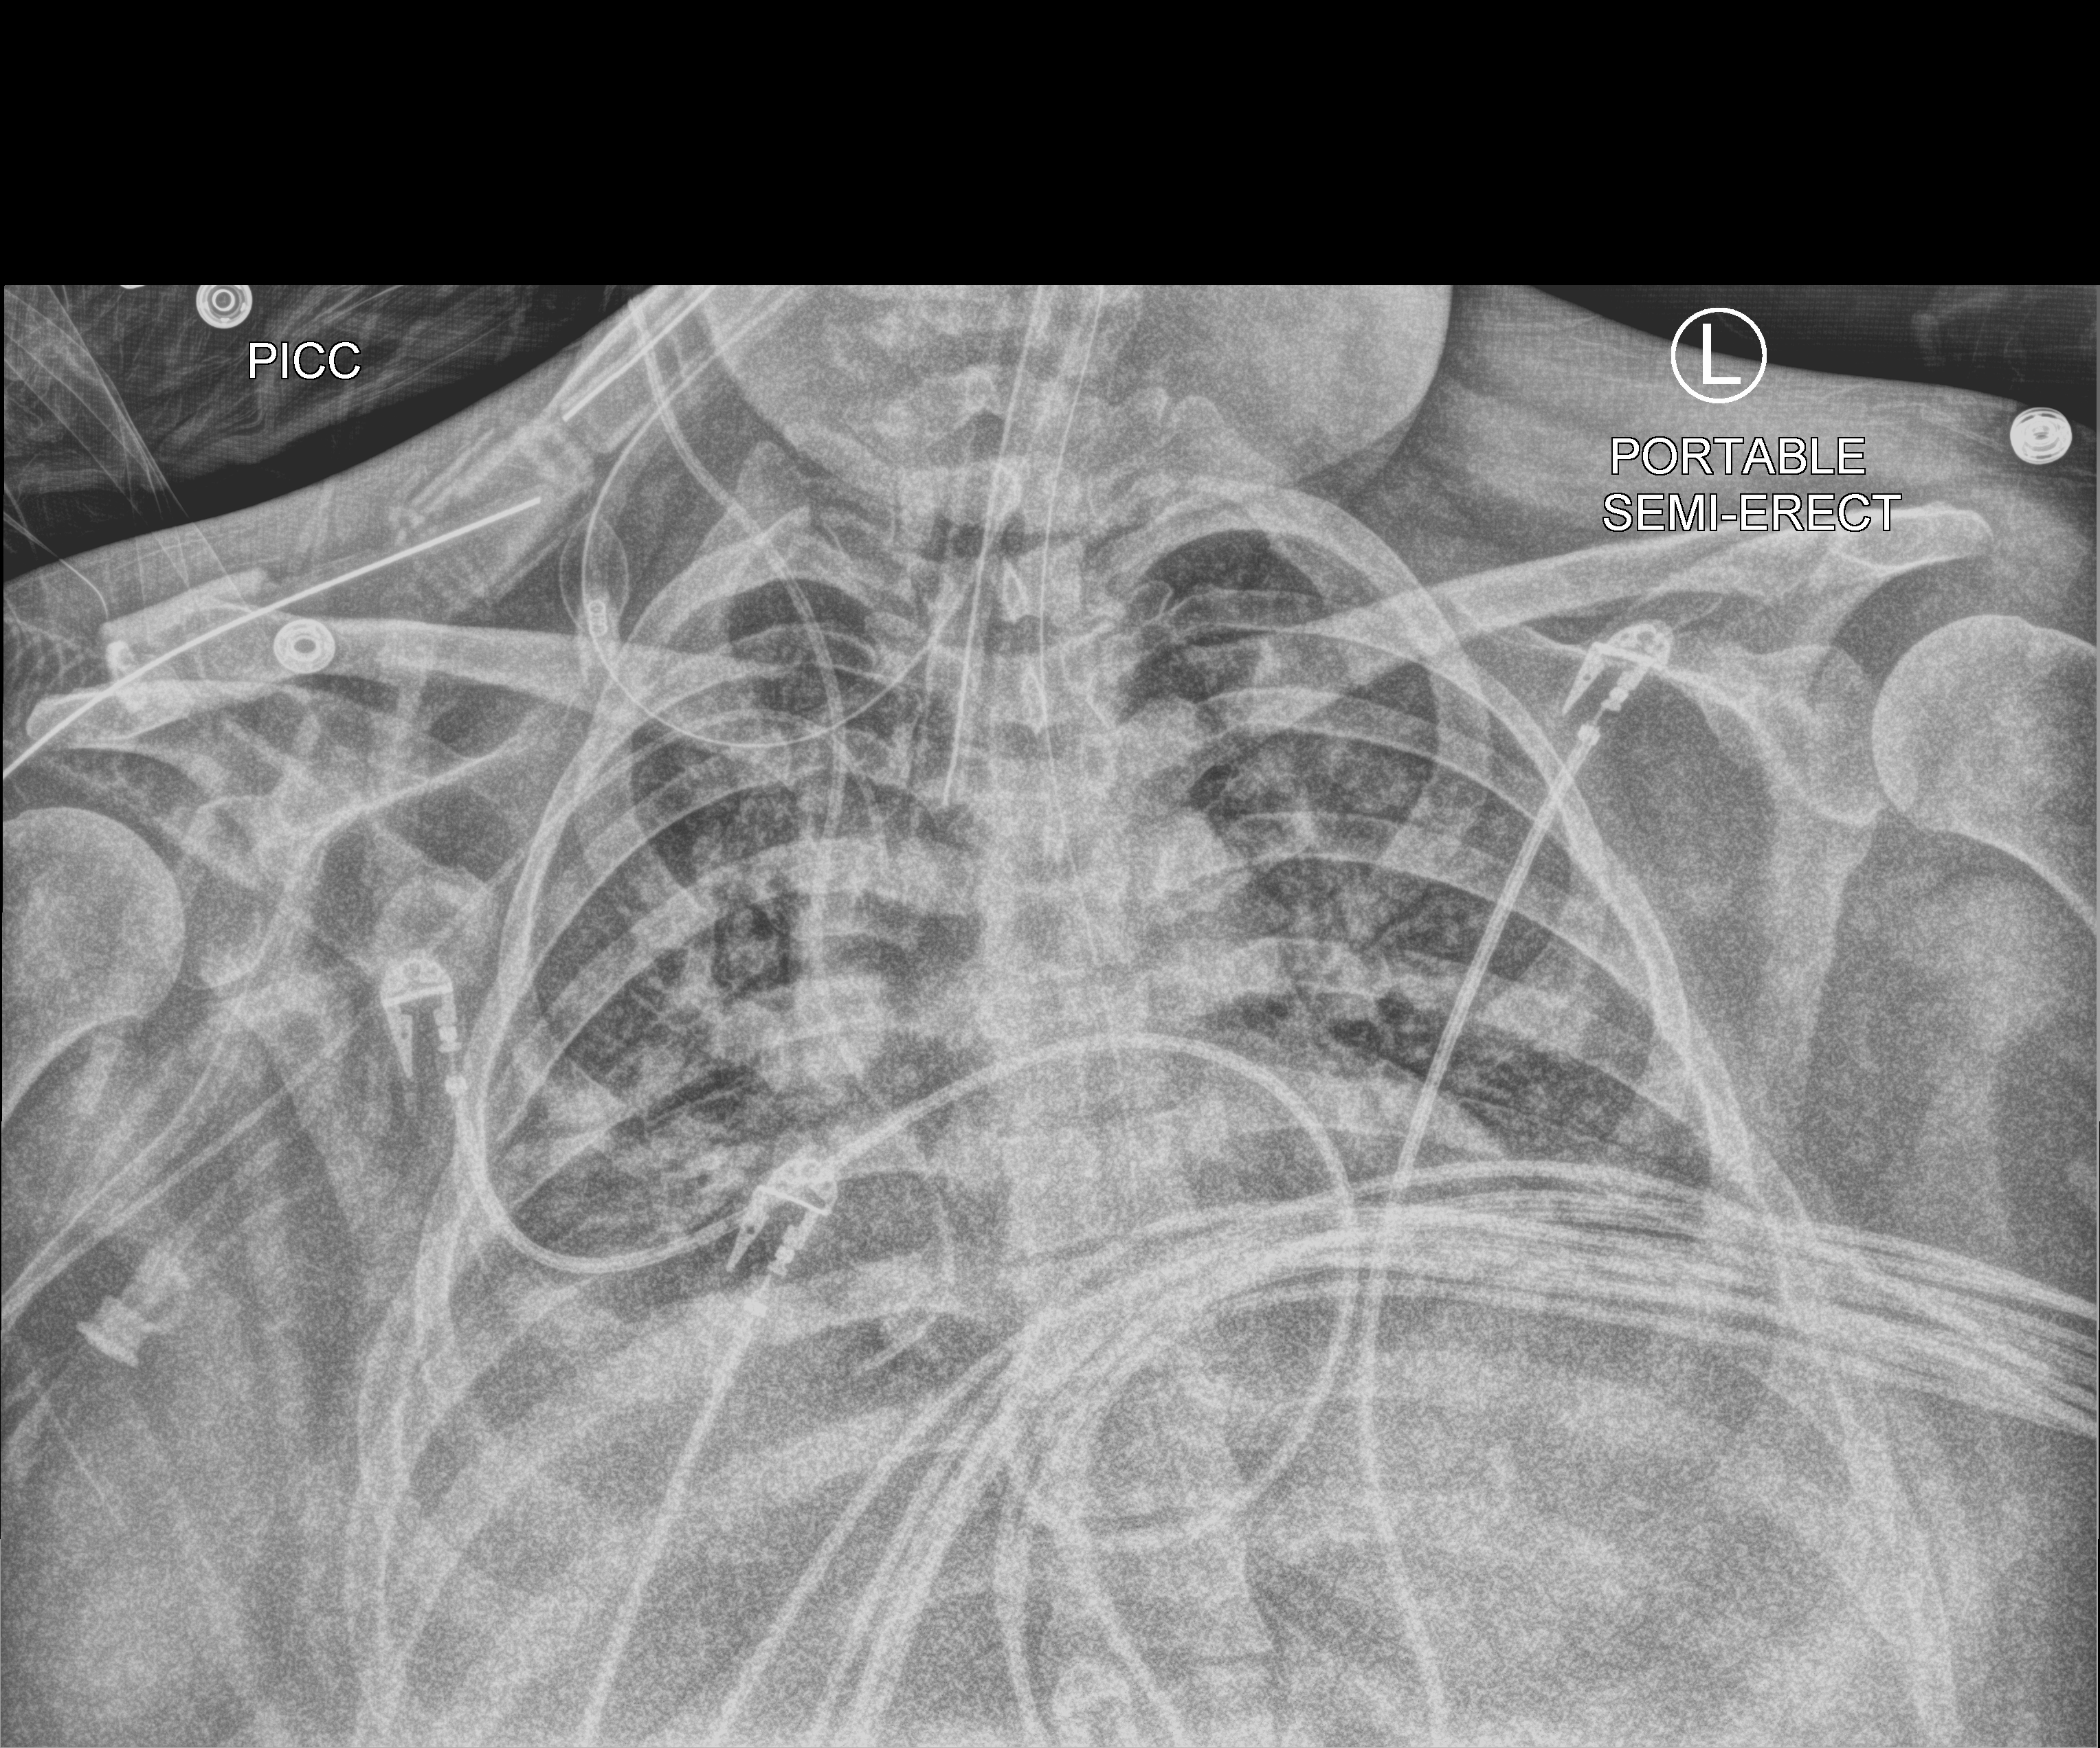
Bedside chest radiograph (computed radiography). Female patient hospitalised with COVID-19, age 18–59 years.
Admission-level facts for this patient (not findings on this image; timing relative to this image not recorded):
- COPD (admission record): no
- admitted to intensive care during this hospital stay: yes
- mechanically ventilated during this hospital stay: yes